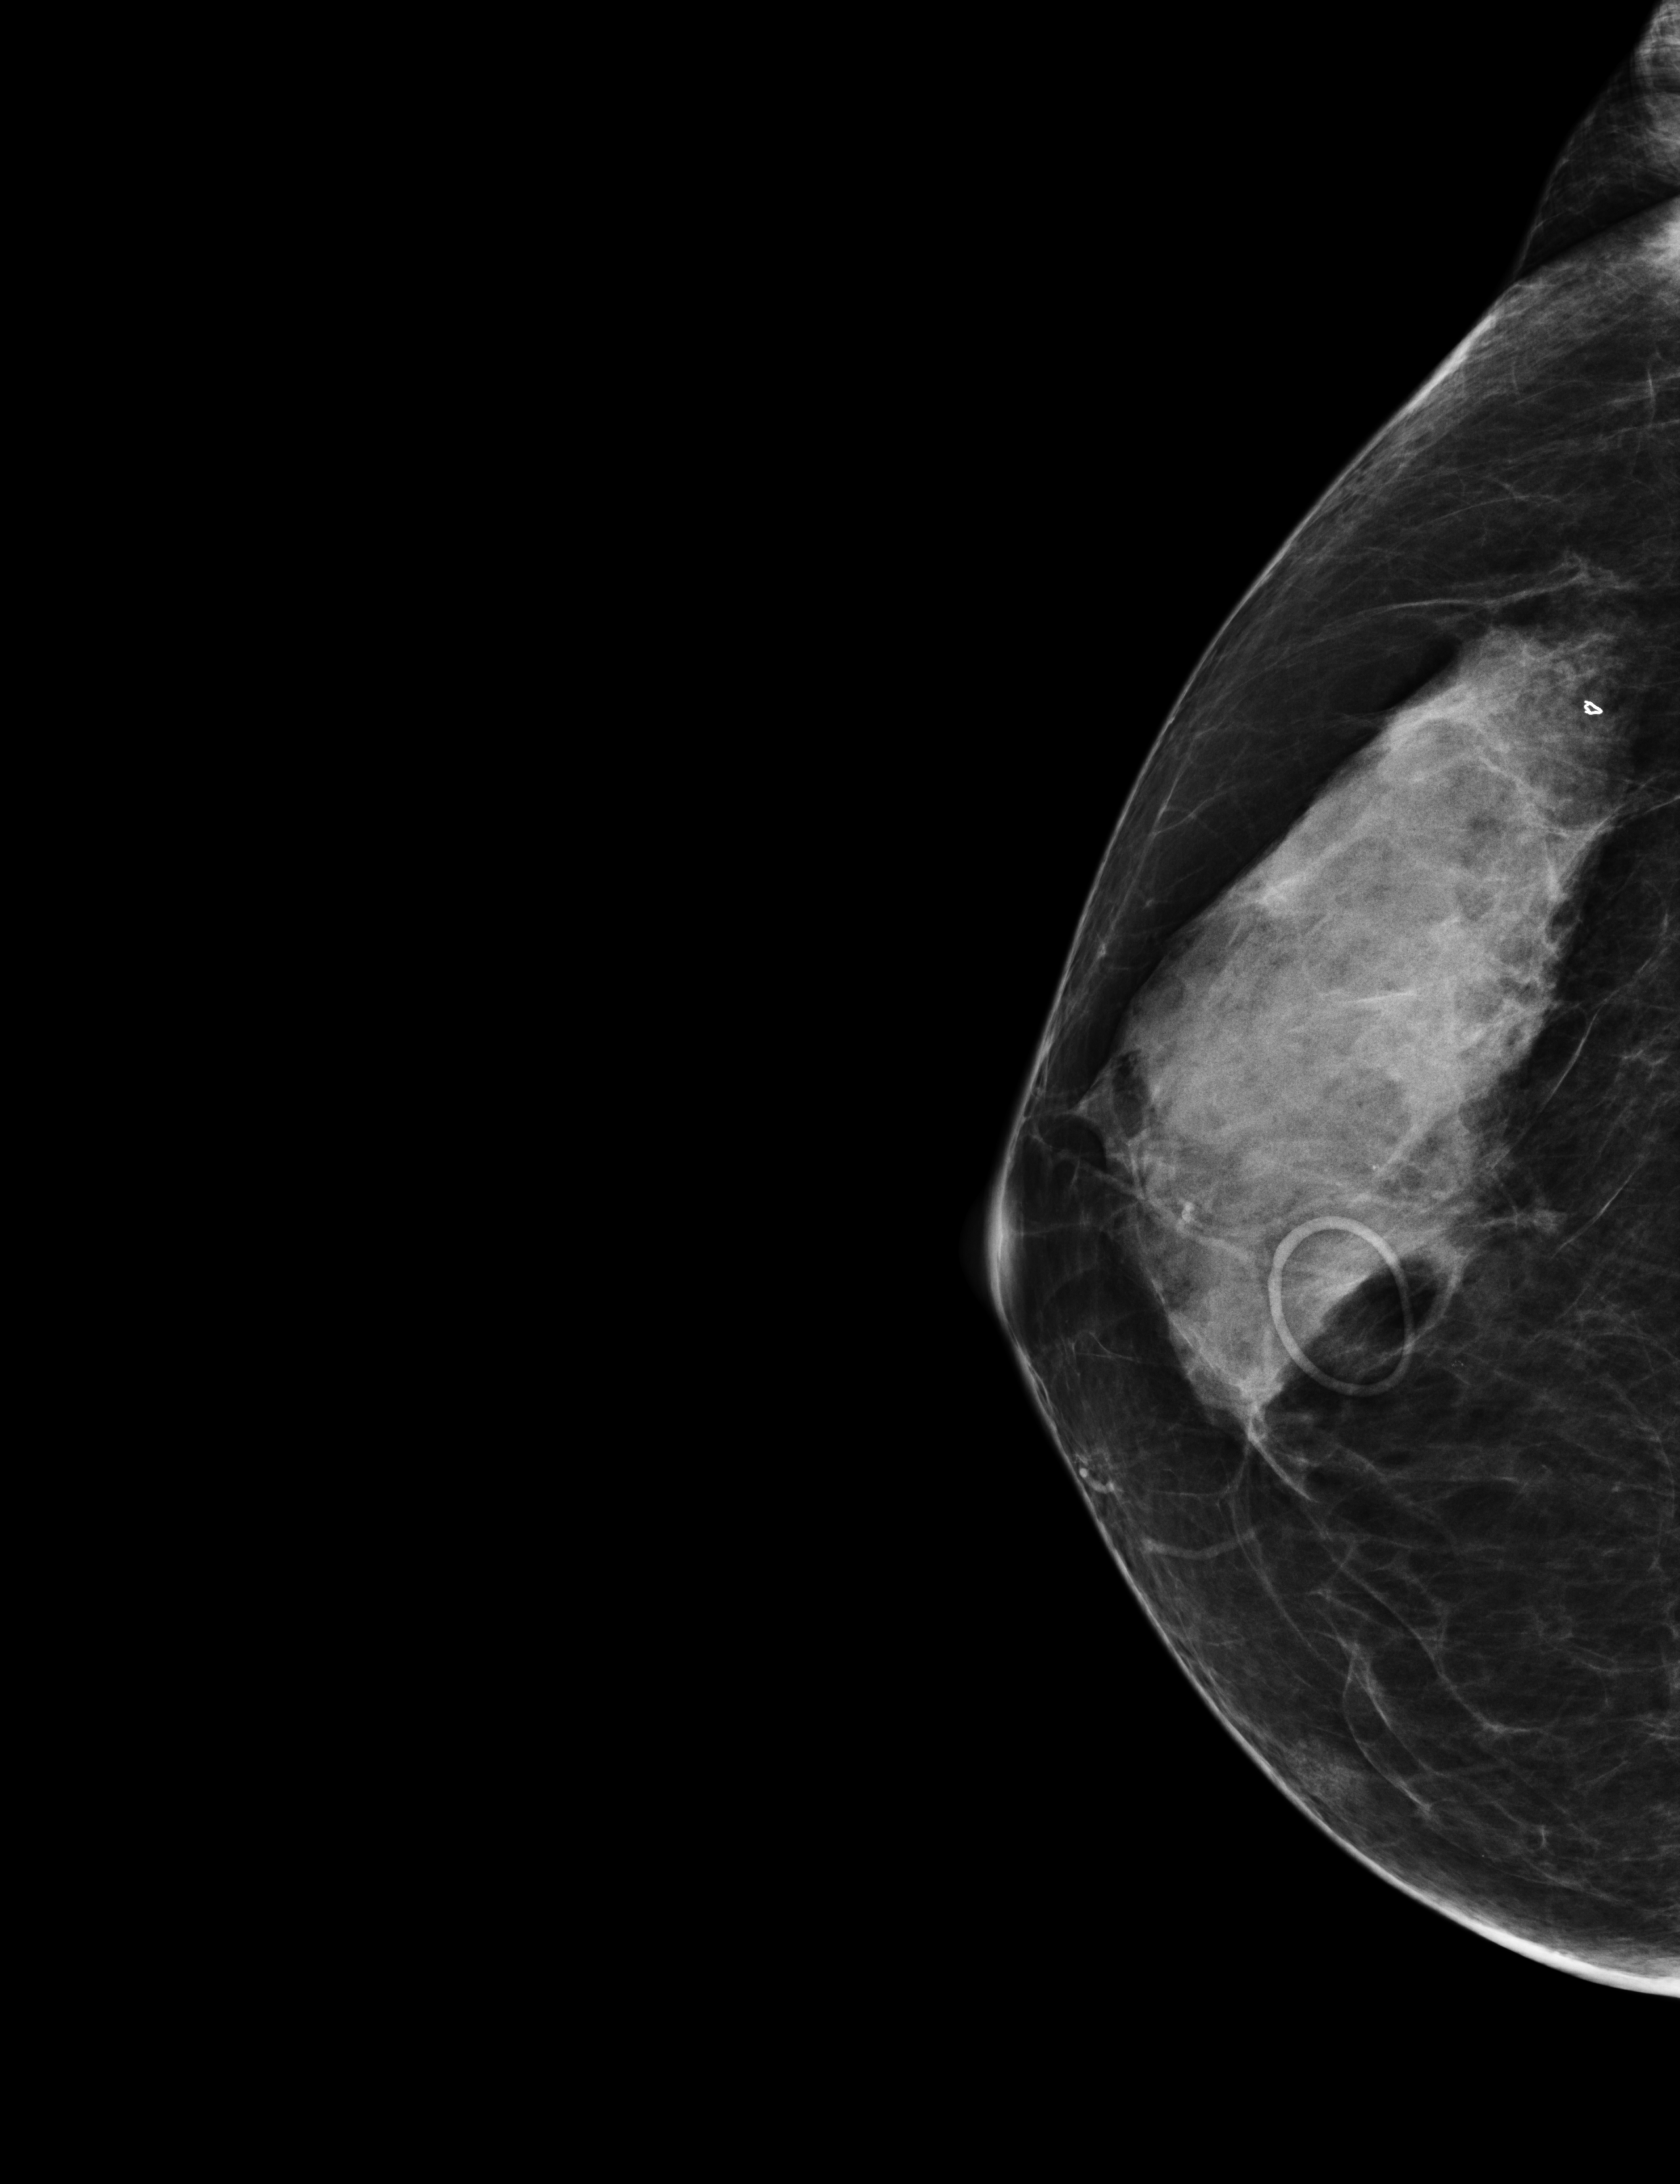
Full-field digital mammogram (FFDM); right breast; craniocaudal (CC) view; screening examination; compressed breast thickness 52 mm. Patient: female, 66 years.
Final BI-RADS category for the screening round (tomosynthesis exam, both breasts): category 1.